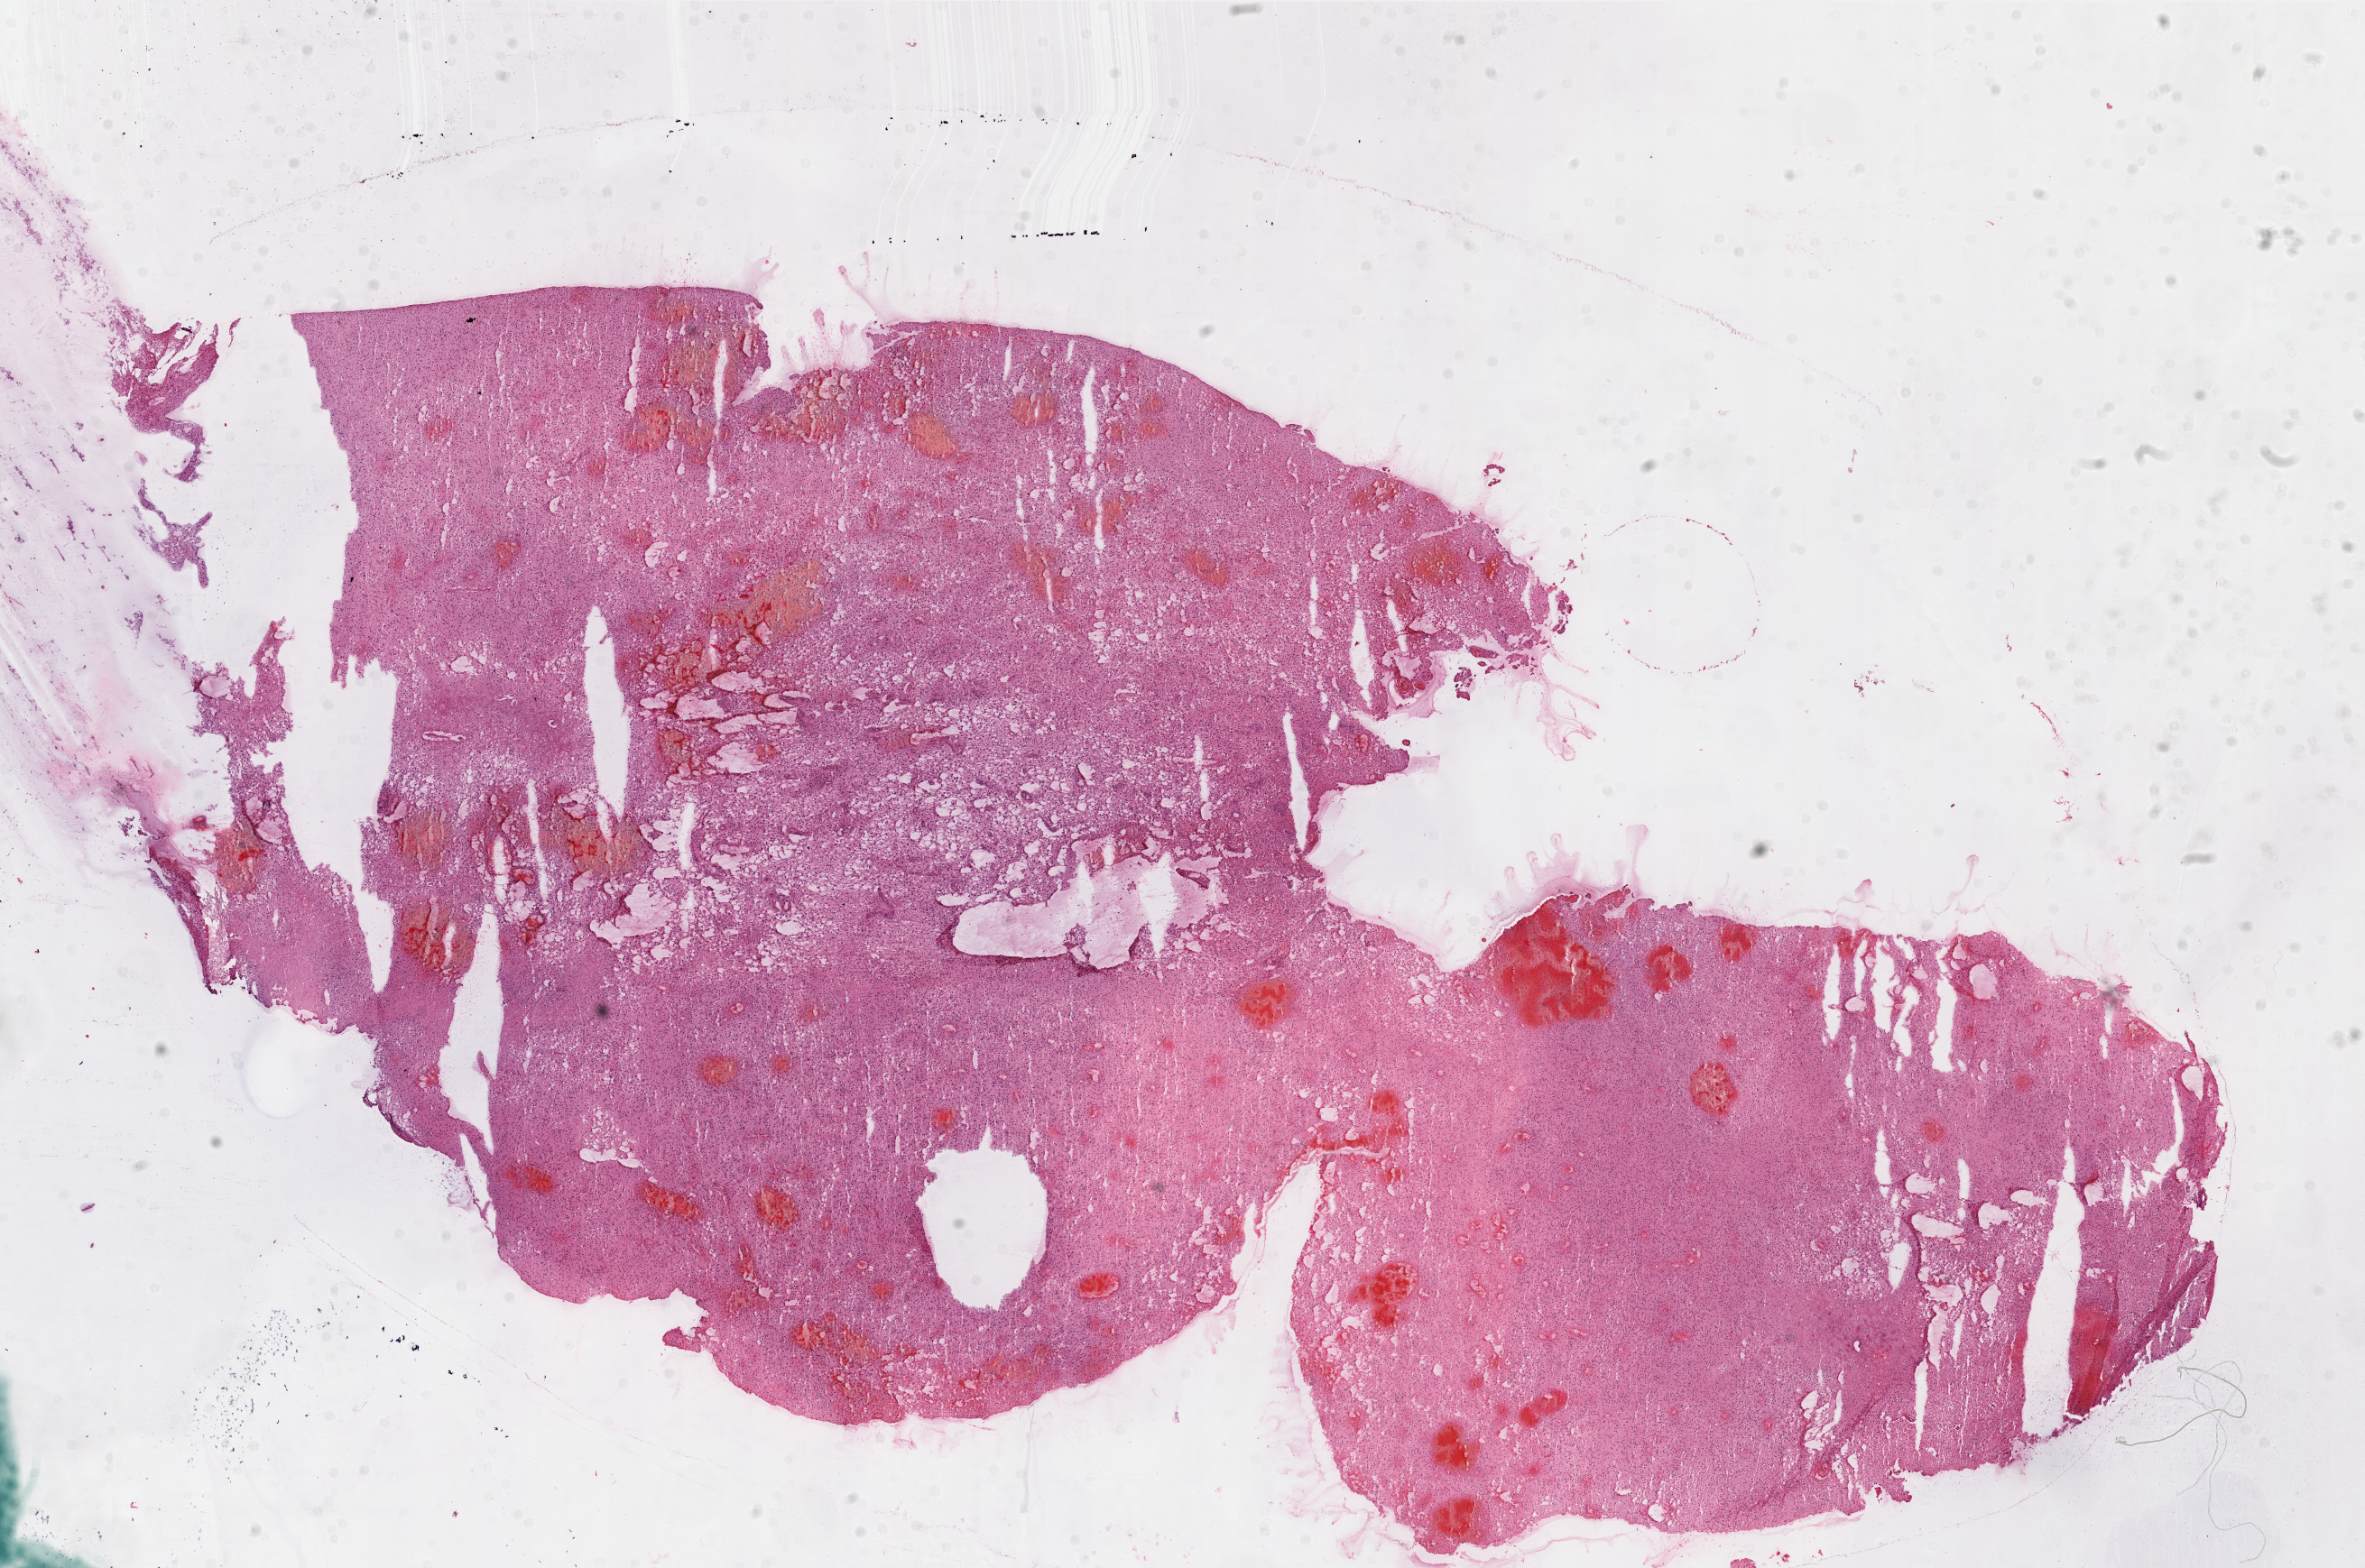
Digitized H&E-stained tissue section (whole slide) — shown as a low-resolution overview of the whole scanned area (about 21.0 x 13.9 mm, slide scanned at 20x). Frozen section from the top of the tissue portion. Primary tumour sample from the brain. Male, age 52 years at initial diagnosis. Pathologist review of this section (percent, as recorded): tumour cells 90%, tumour nuclei 100%, normal cells 0%, stromal cells 0%, necrosis 10%.
Histologic diagnosis: Glioblastoma.